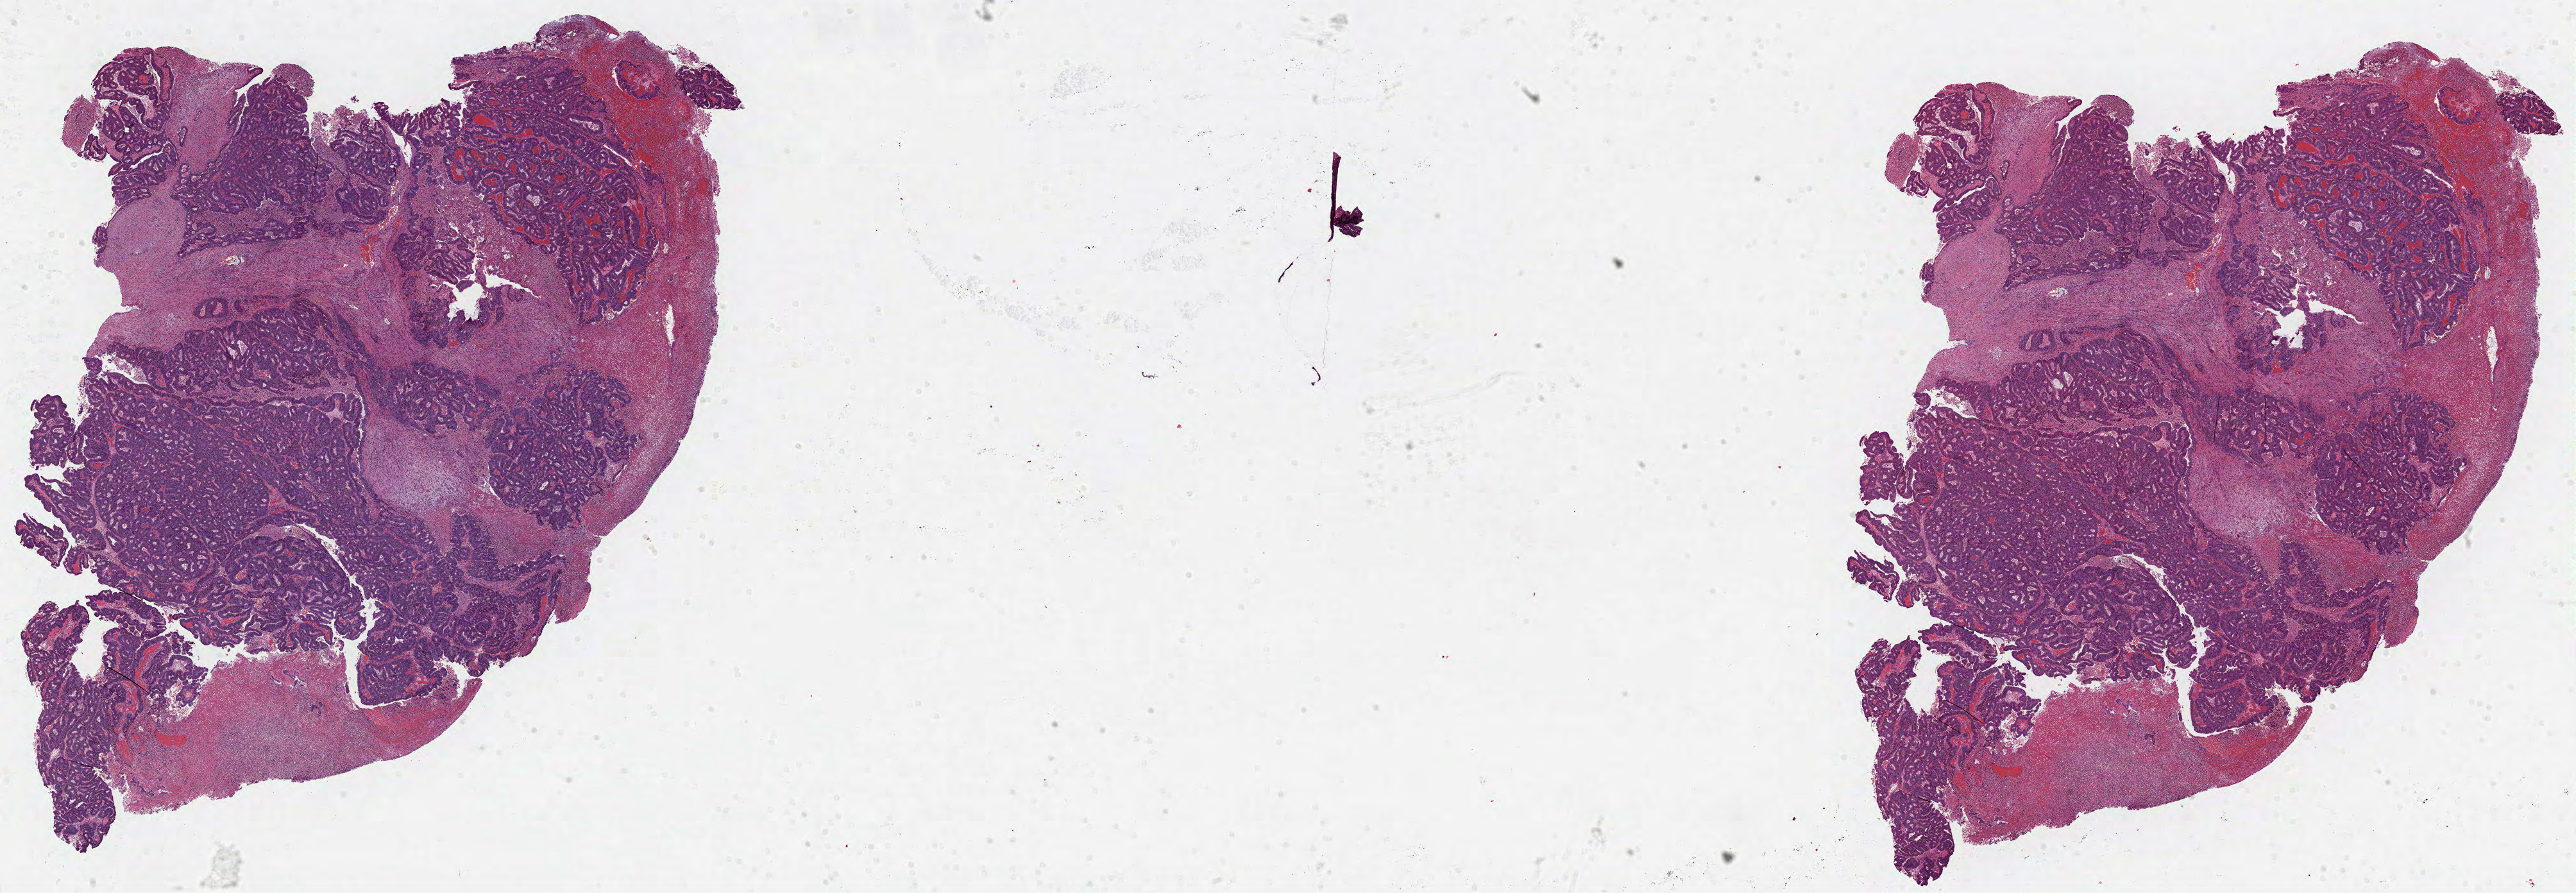
Whole-slide histology image, Hematoxylin and eosin (H&E) stained — low-resolution overview of the scanned area, about 32.4 x 11.2 mm (slide scanned at 40x). Formalin-fixed paraffin-embedded (FFPE) diagnostic section. Primary tumour sample from the colon. Patient: male, age at initial diagnosis 78 years.
* AJCC pathologic stage: IIC
* pathologic diagnosis: Adenocarcinoma, NOS